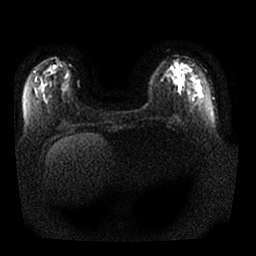
Breast MRI, one axial slice; diffusion-weighted series; image 2 of 4 stored at this slice position (different b-values; order by instance number); 1.5 T; 4 mm slice thickness; 256 × 256 image matrix, field of view 350 × 350 mm. Female patient.
Outlined on this slice (expert manual segmentation):
- tumour on diffusion-weighted imaging: bounding box <171,66,180,77> (left, top, right, bottom; pixels)